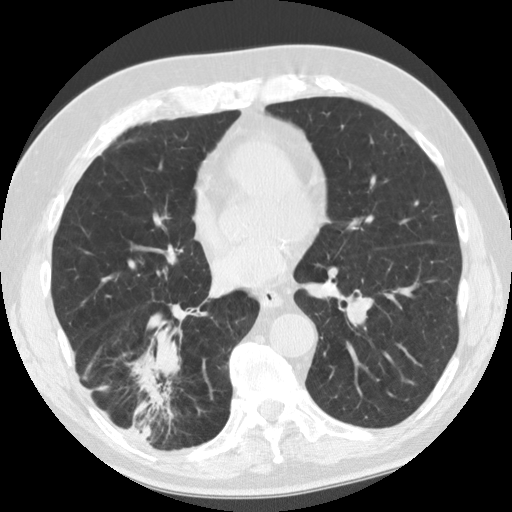
Low-dose screening chest CT, one axial slice. Position 53 of 135 along the scan axis. Reconstruction kernel STANDARD. Lung window (W 1500 / L -600 HU). 2.5 mm slice thickness. 512 × 512 image matrix, field of view 340 × 340 mm.
Structures marked on this image (manually delineated by an expert):
- lesion 1 (tumor, lower lobe of right lung): bounding box [x1, y1, x2, y2] px = [129, 326, 182, 439]